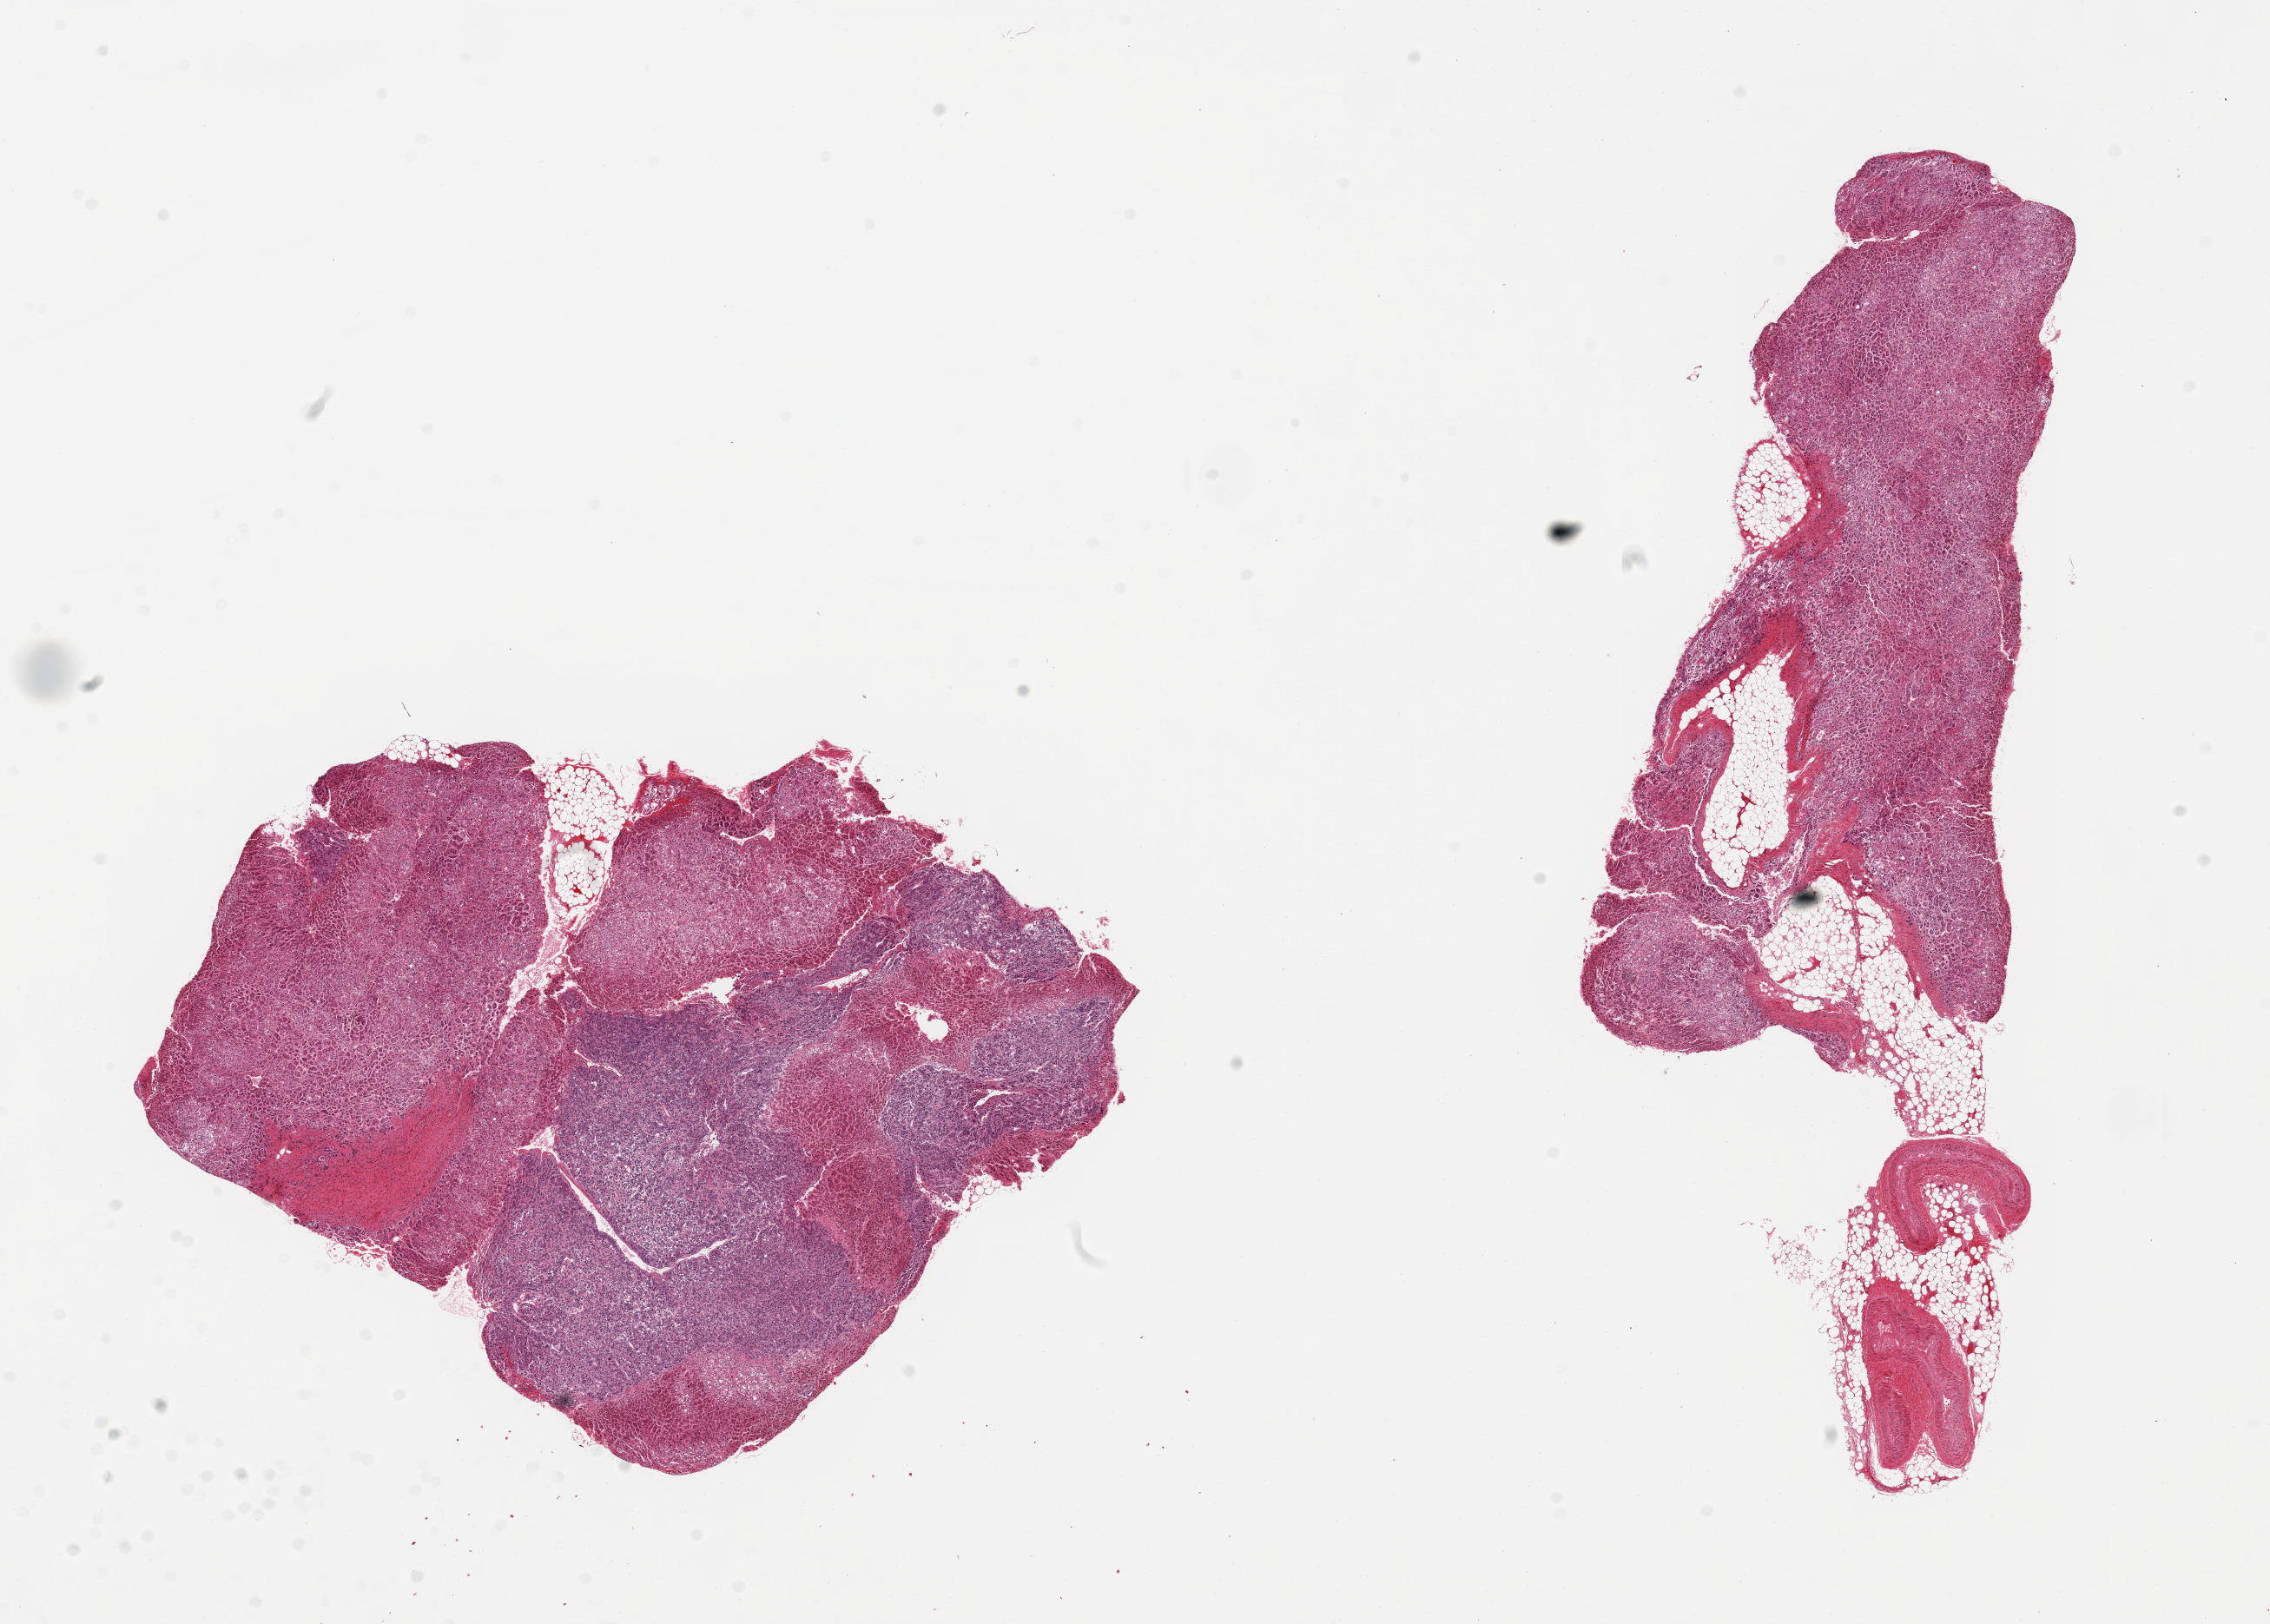
Digitized H&E-stained section, low-resolution overview of the scanned area, about 20.7 x 14.8 mm (from a 20x scan), PAXgene-fixed, paraffin-embedded tissue, target tissue: adrenal gland, donor tissue sample. Donor: male.
Pathologist's review note for this sample: 2 pieces, mainly cortex, ~3mm focus of medulla, moderately/markedly autolyzed.